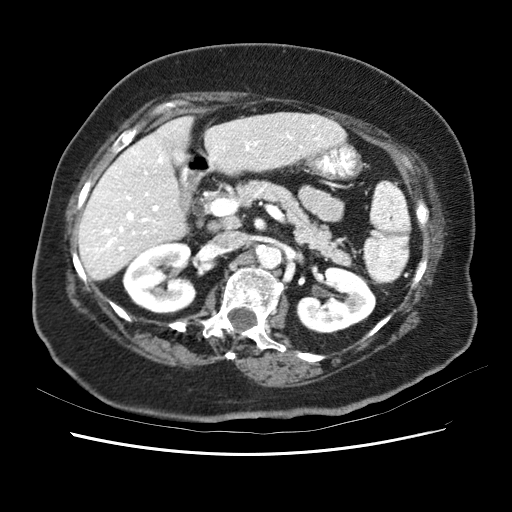
Contrast-enhanced abdominal CT (liver protocol), one axial slice; position 26 of 62 along the scan axis; 120 kVp; soft-tissue window (W 400 / L 40 HU); 2.5 mm slice thickness; 512 × 512 image matrix, field of view 340 × 340 mm. From the clinical record (not read from this slice): diagnosis: hepatocellular carcinoma (patient treated with transarterial chemoembolisation; whether this scan precedes or follows treatment is not stated here); TNM stage (as recorded): Stage-I.
Annotated regions visible in this slice (semi-automatically segmented with operator editing):
- liver parenchyma outside the tumour (the mass and vessels are separate outlines, so this box may not span the whole liver): box from (x=78, y=112) to (x=350, y=282) px
- liver vessels: (x=82, y=120)–(x=314, y=263)